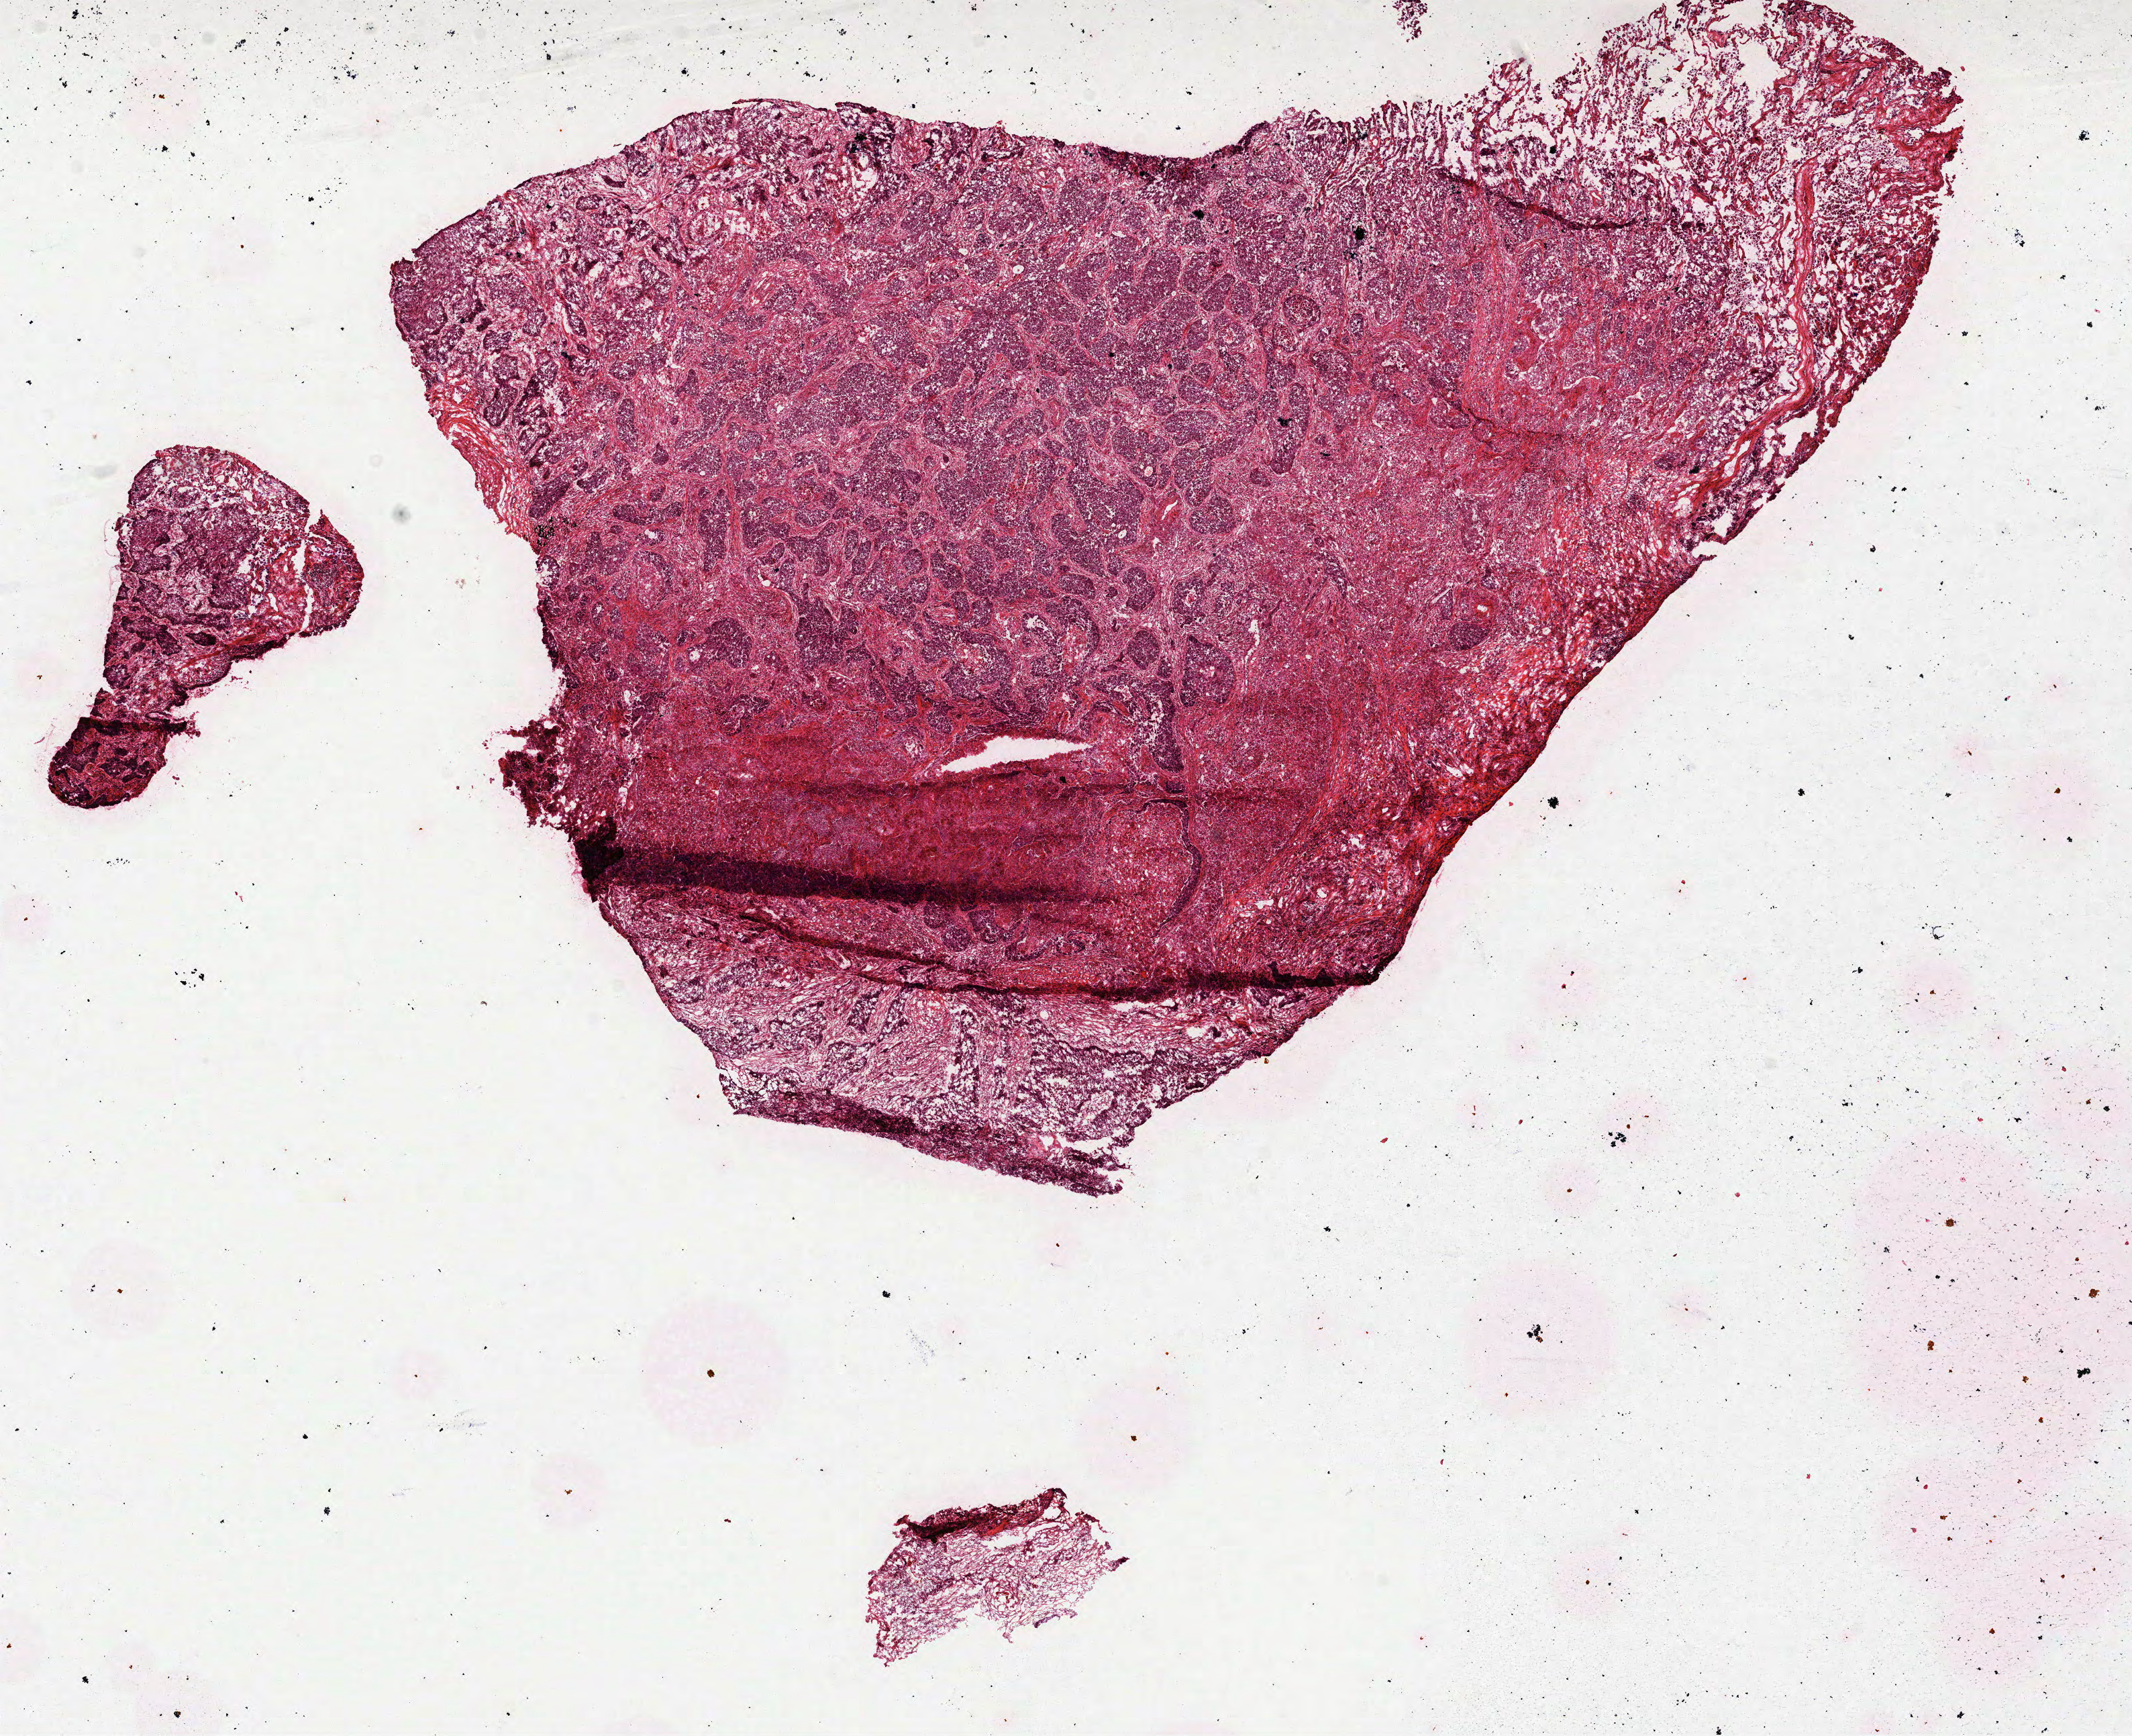
Whole-slide histology image, H&E-stained, a low-resolution overview of the entire scanned area, about 12.8 x 10.4 mm (acquisition: 40x scan); formalin-fixed paraffin-embedded (FFPE) diagnostic section; sample: primary tumour, lung. Patient: male, age at initial diagnosis 73 years.
* AJCC pathologic stage: IB (7th edition)
* diagnosis: Squamous cell carcinoma, NOS (upper lobe, lung)
* laterality: left